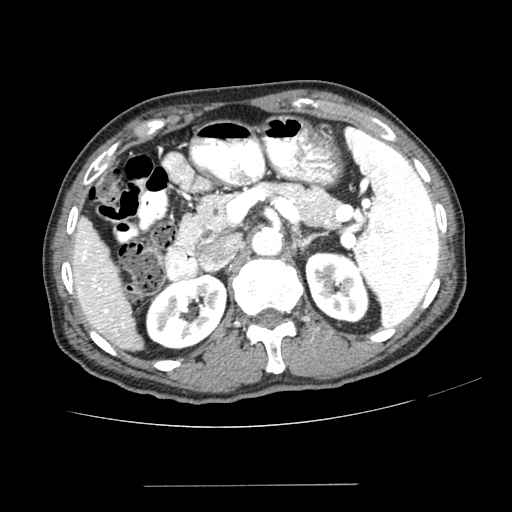
Contrast-enhanced abdominal CT (liver protocol), one axial slice; position 143 of 187 along the scan axis; reconstruction kernel SOFT; one of 2 acquisitions stored at this slice position; soft-tissue window (W 400 / L 40 HU); 512 × 512 image matrix. Case-level facts recorded for this patient, not image findings: diagnosis: hepatocellular carcinoma (patient treated with transarterial chemoembolisation; whether this scan precedes or follows treatment is not stated here); TNM stage (as recorded): Stage-I; Child-Pugh class: A; tumour differentiation: poorly differentiated; tumour size: 1.6 cm.
Outlined on this slice (semi-automatically segmented with operator editing):
- liver parenchyma outside the tumour (the mass and vessels are separate outlines, so this box may not span the whole liver): bounding box <70,216,142,350> (left, top, right, bottom; pixels)
- liver vessels: <79,240,124,327>